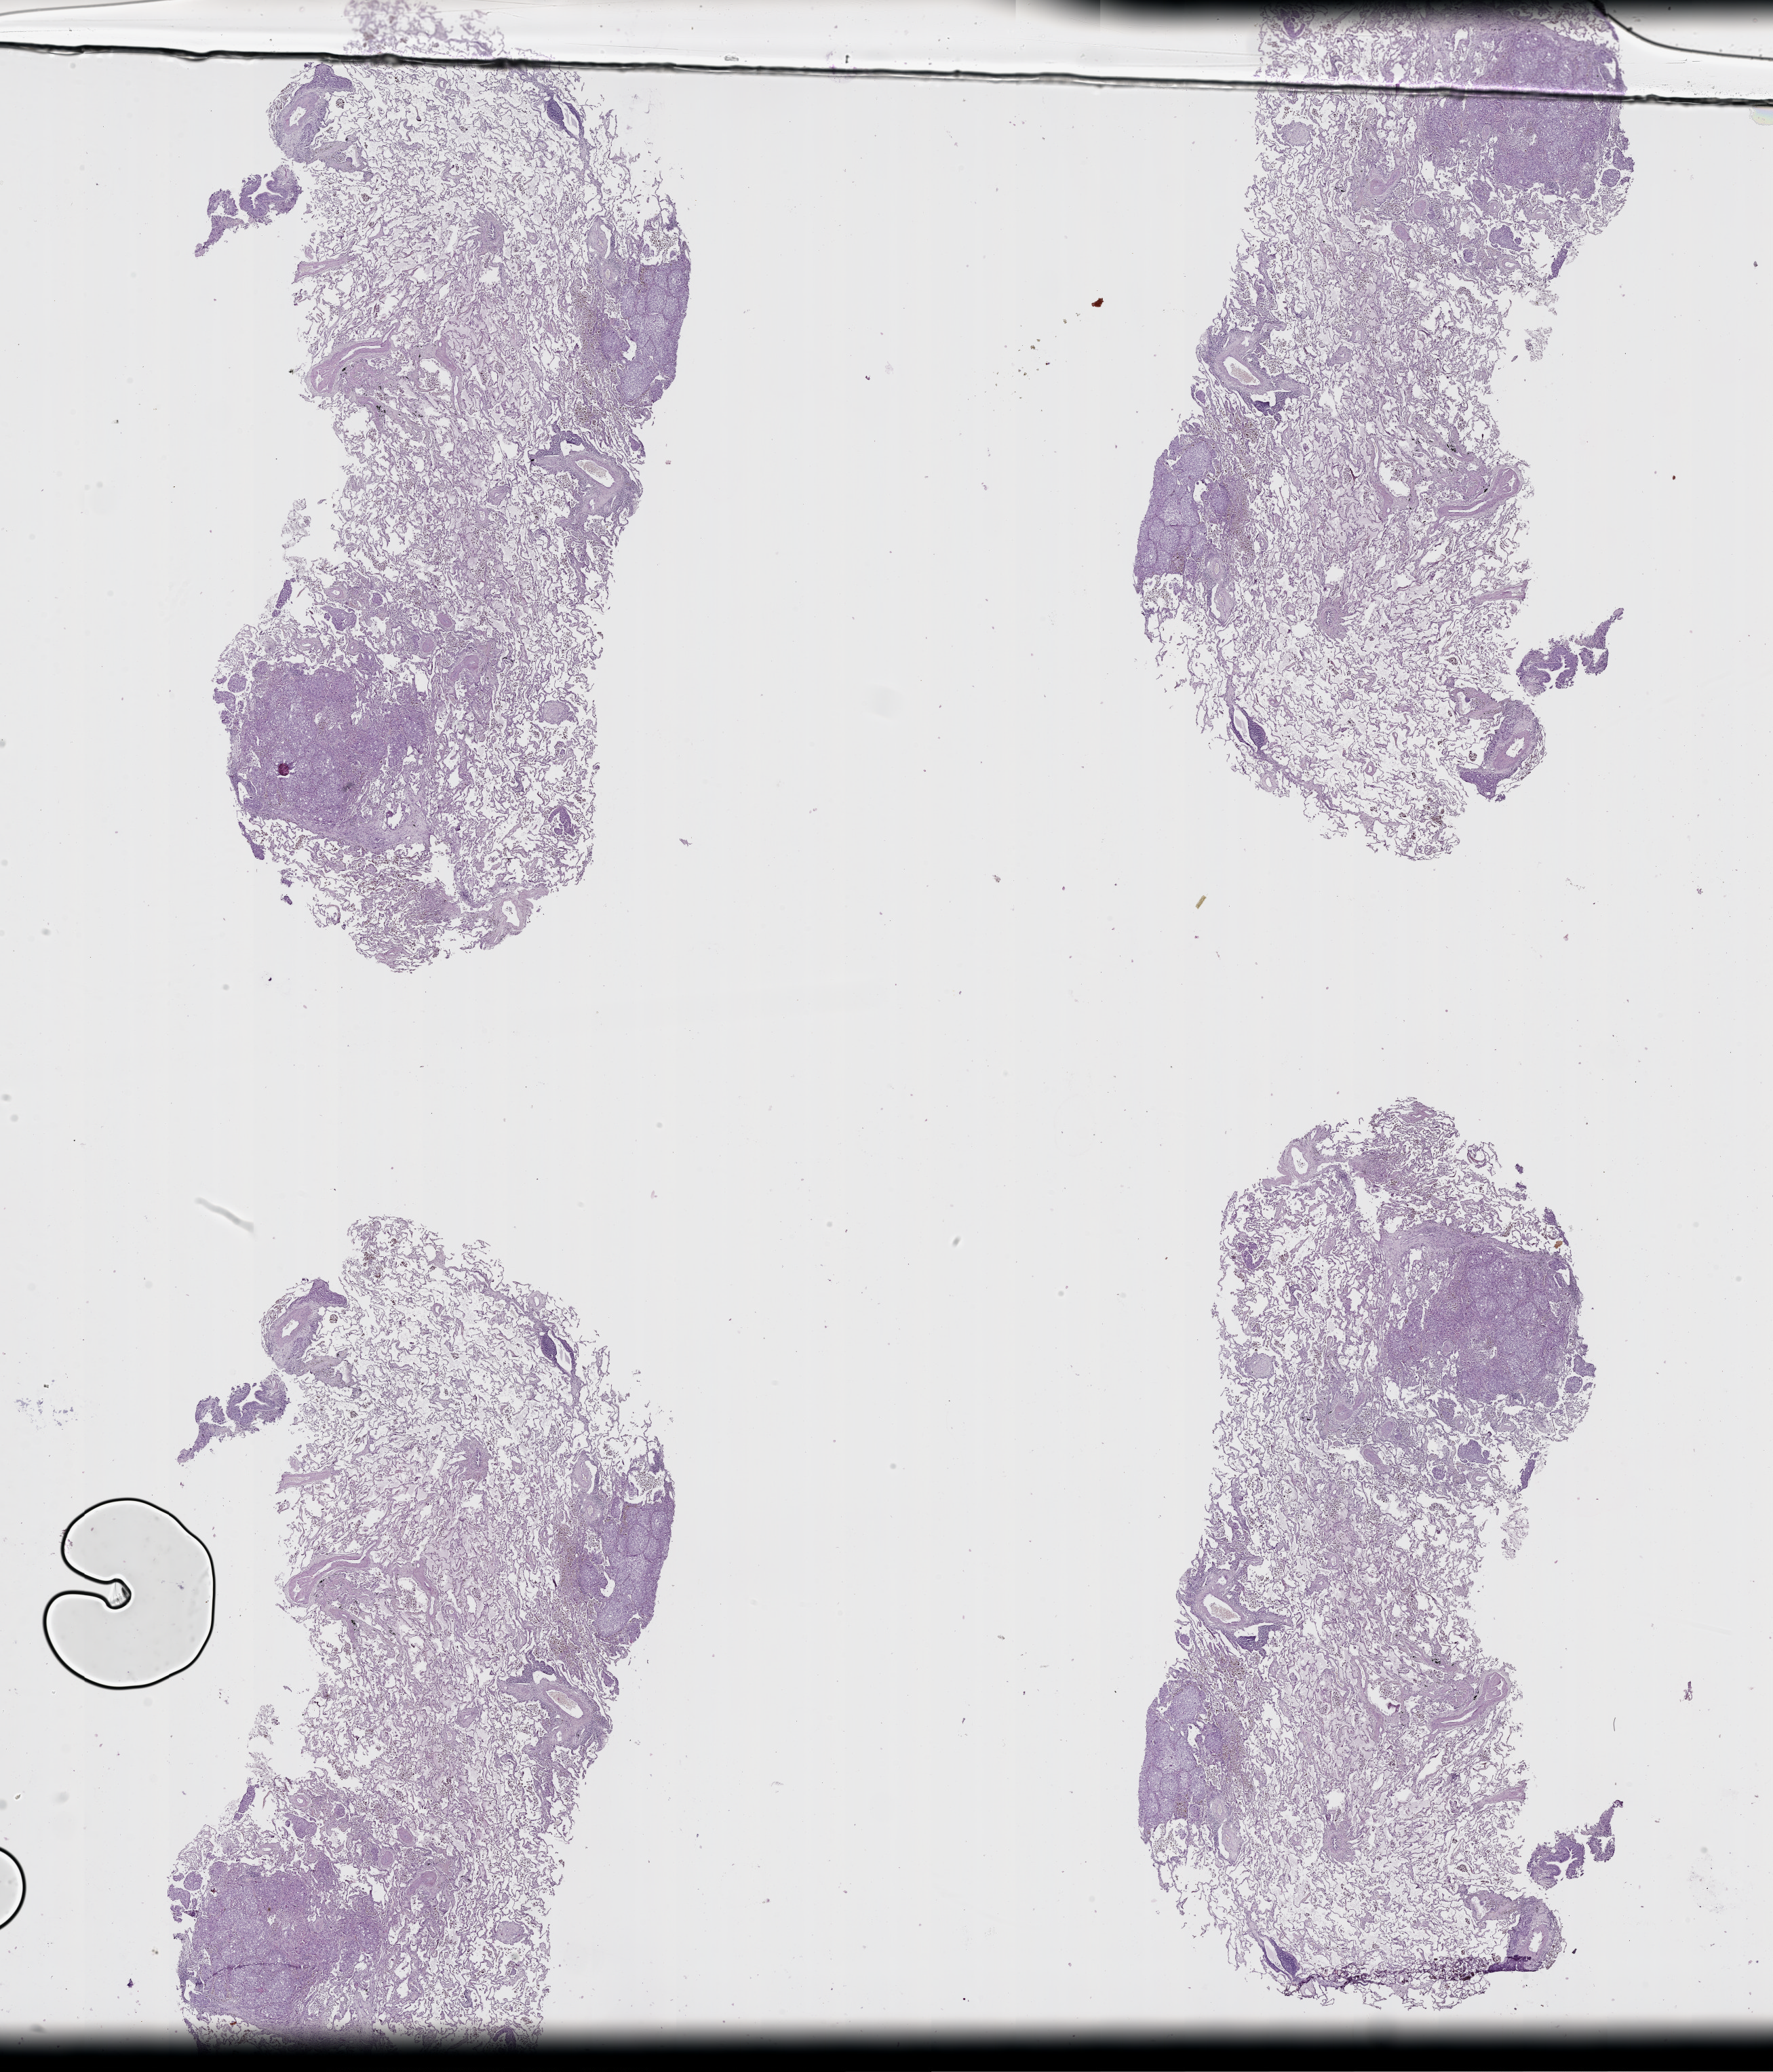
Digitized H&E tissue section (whole slide), low-resolution overview of the scanned area, about 21.0 x 24.6 mm; lung, tissue type not recorded.
Patient diagnosis (cohort enrolment): lung adenocarcinoma (lung).